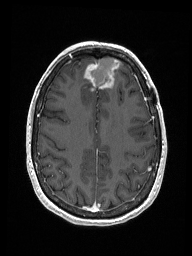
Brain MRI from a brain-tumour surgery series, one axial slice. T1-weighted post-contrast. 1 mm slice thickness. 192 × 256 image matrix. Case-level facts recorded for this patient, not image findings: histopathology: Metastastic Carcinoma from Breast primary; tumour location: Right Frontal.
Outlined on this slice (expert manual segmentation):
- previous resection cavity: bounding box <91,58,118,86> (left, top, right, bottom; pixels)